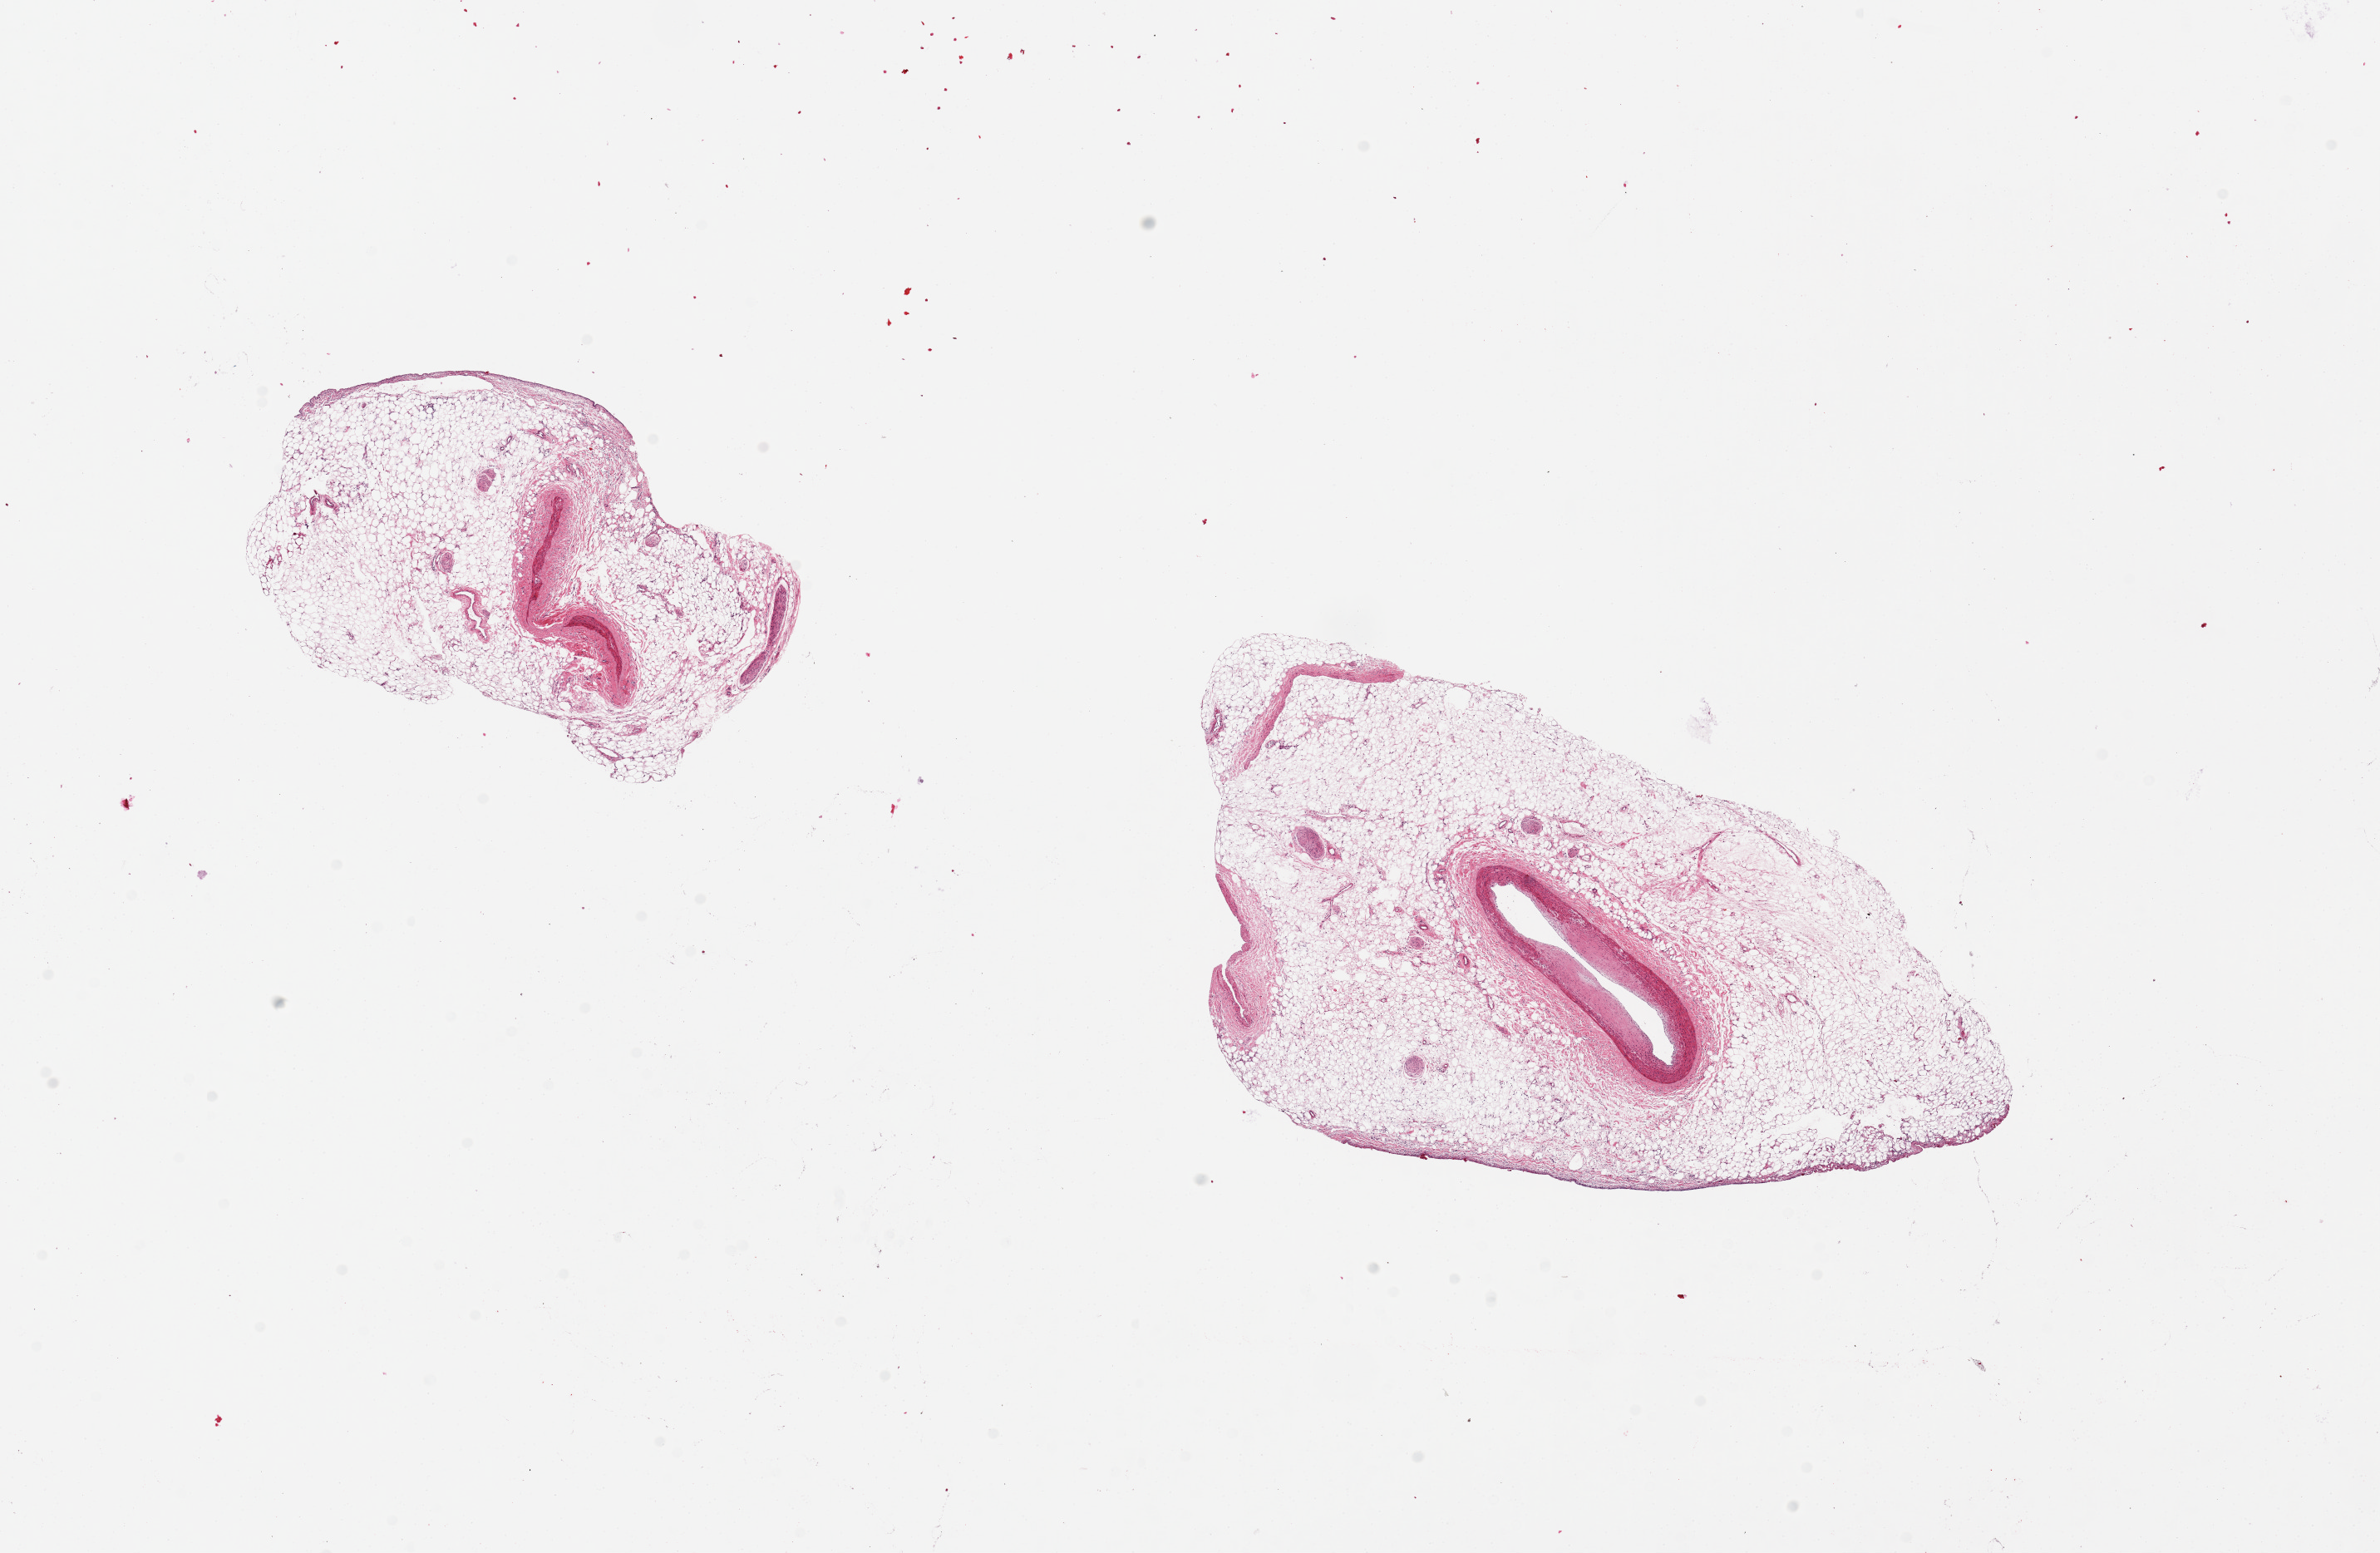
Haematoxylin and eosin whole-slide image — shown as a low-resolution overview of the whole scanned area (about 22.6 x 14.8 mm, acquisition: 20x scan), PAXgene-fixed, paraffin-embedded tissue, target tissue: coronary artery, donor tissue sample.
• pathologist's review note for this sample: 2 pieces. 5x3 & 9x5mm; 90% adipose. Small artery with plaque in one and very small artery in other